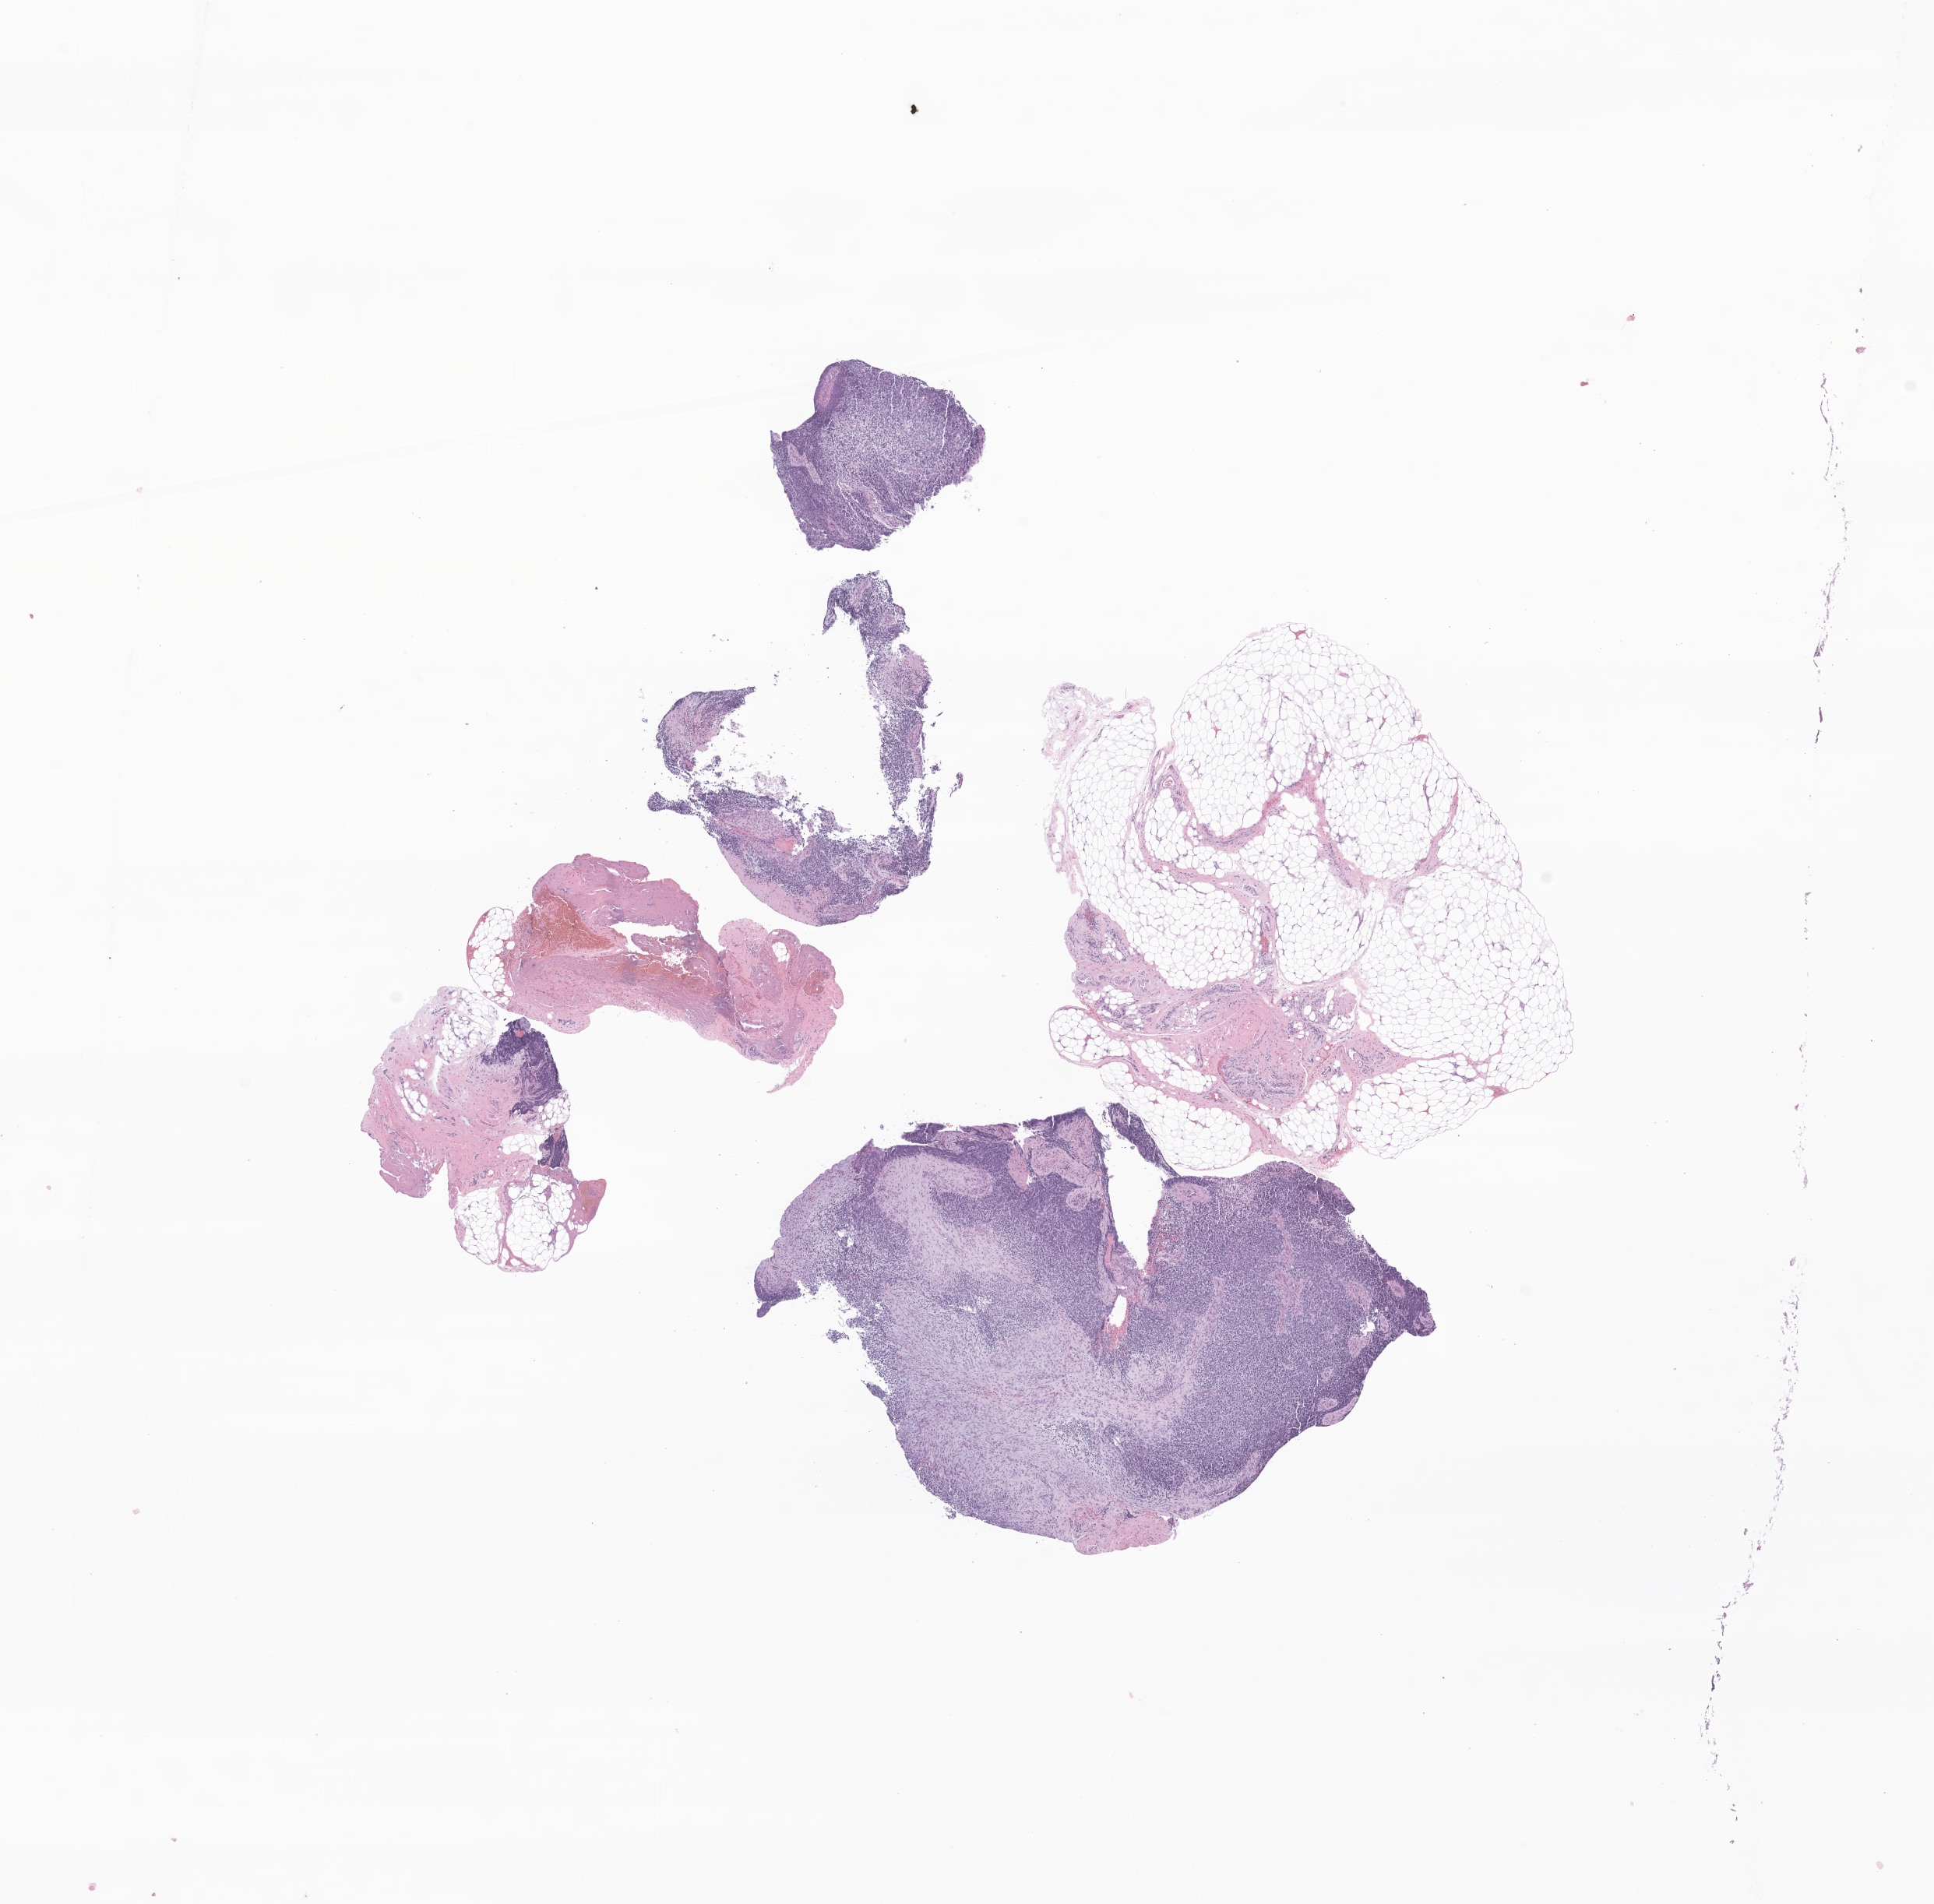
Haematoxylin and eosin whole-slide image of tumor tissue from the orbit — whole scanned area (about 10.5 x 10.3 mm) shown as a low-resolution overview, FFPE section. Patient: female, age 396 days.
- recorded diagnosis: Embryonal rhabdomyosarcoma, NOS